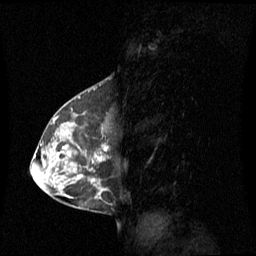
Breast MRI (dynamic contrast-enhanced), one sagittal slice; slice 33 of 60 in the series (ordered by position); dynamic contrast-enhanced series, image 2 of 3 at this slice position (ordered by acquisition); 1.5 T; TE 4.2 ms, TR 8.4 ms; 2 mm slice thickness; 256 × 256 image matrix, field of view 270 × 270 mm. Female patient, age 42 years. Case-level facts recorded for this patient, not image findings: setting: breast cancer imaged before/during neoadjuvant chemotherapy; receptor status: HR-positive, HER2-negative.
Outlined on this slice (semi-automatic segmentation, software-assisted and operator-edited):
- analysis volume of interest (the breast-tissue region the enhancement analysis was run in; not a lesion): bounding box (x1, y1, x2, y2) in pixels: (56, 113, 109, 185)
- tumour enhancement mask (voxels above the 70 % enhancement threshold inside the analysis volume of interest): (98, 145, 108, 161)